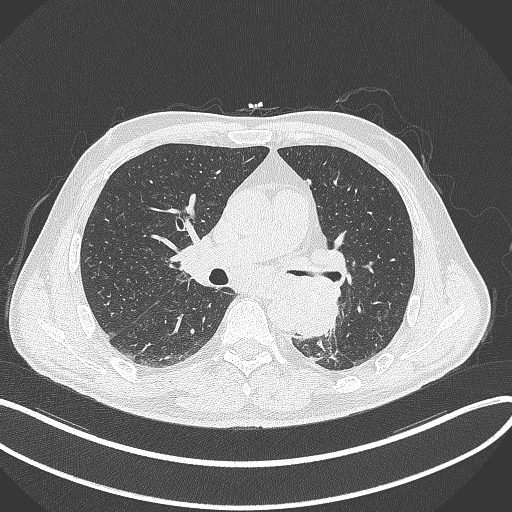
Chest CT, one axial slice; slice 192 of 329 in the series (ordered by position); reconstruction kernel B70f; lung window (W 1500 / L -600 HU); 1 mm slice thickness; 512 × 512 image matrix, field of view 400 × 400 mm. Male patient, age 59 years. From the clinical record (not read from this slice): clinical TNM (as recorded): T2a N2 M0.
Annotated regions visible in this slice (bounding box drawn by a radiologist):
- lung tumour (recorded histology: squamous cell carcinoma): bounding box (x1, y1, x2, y2) in pixels: (285, 273, 341, 342)